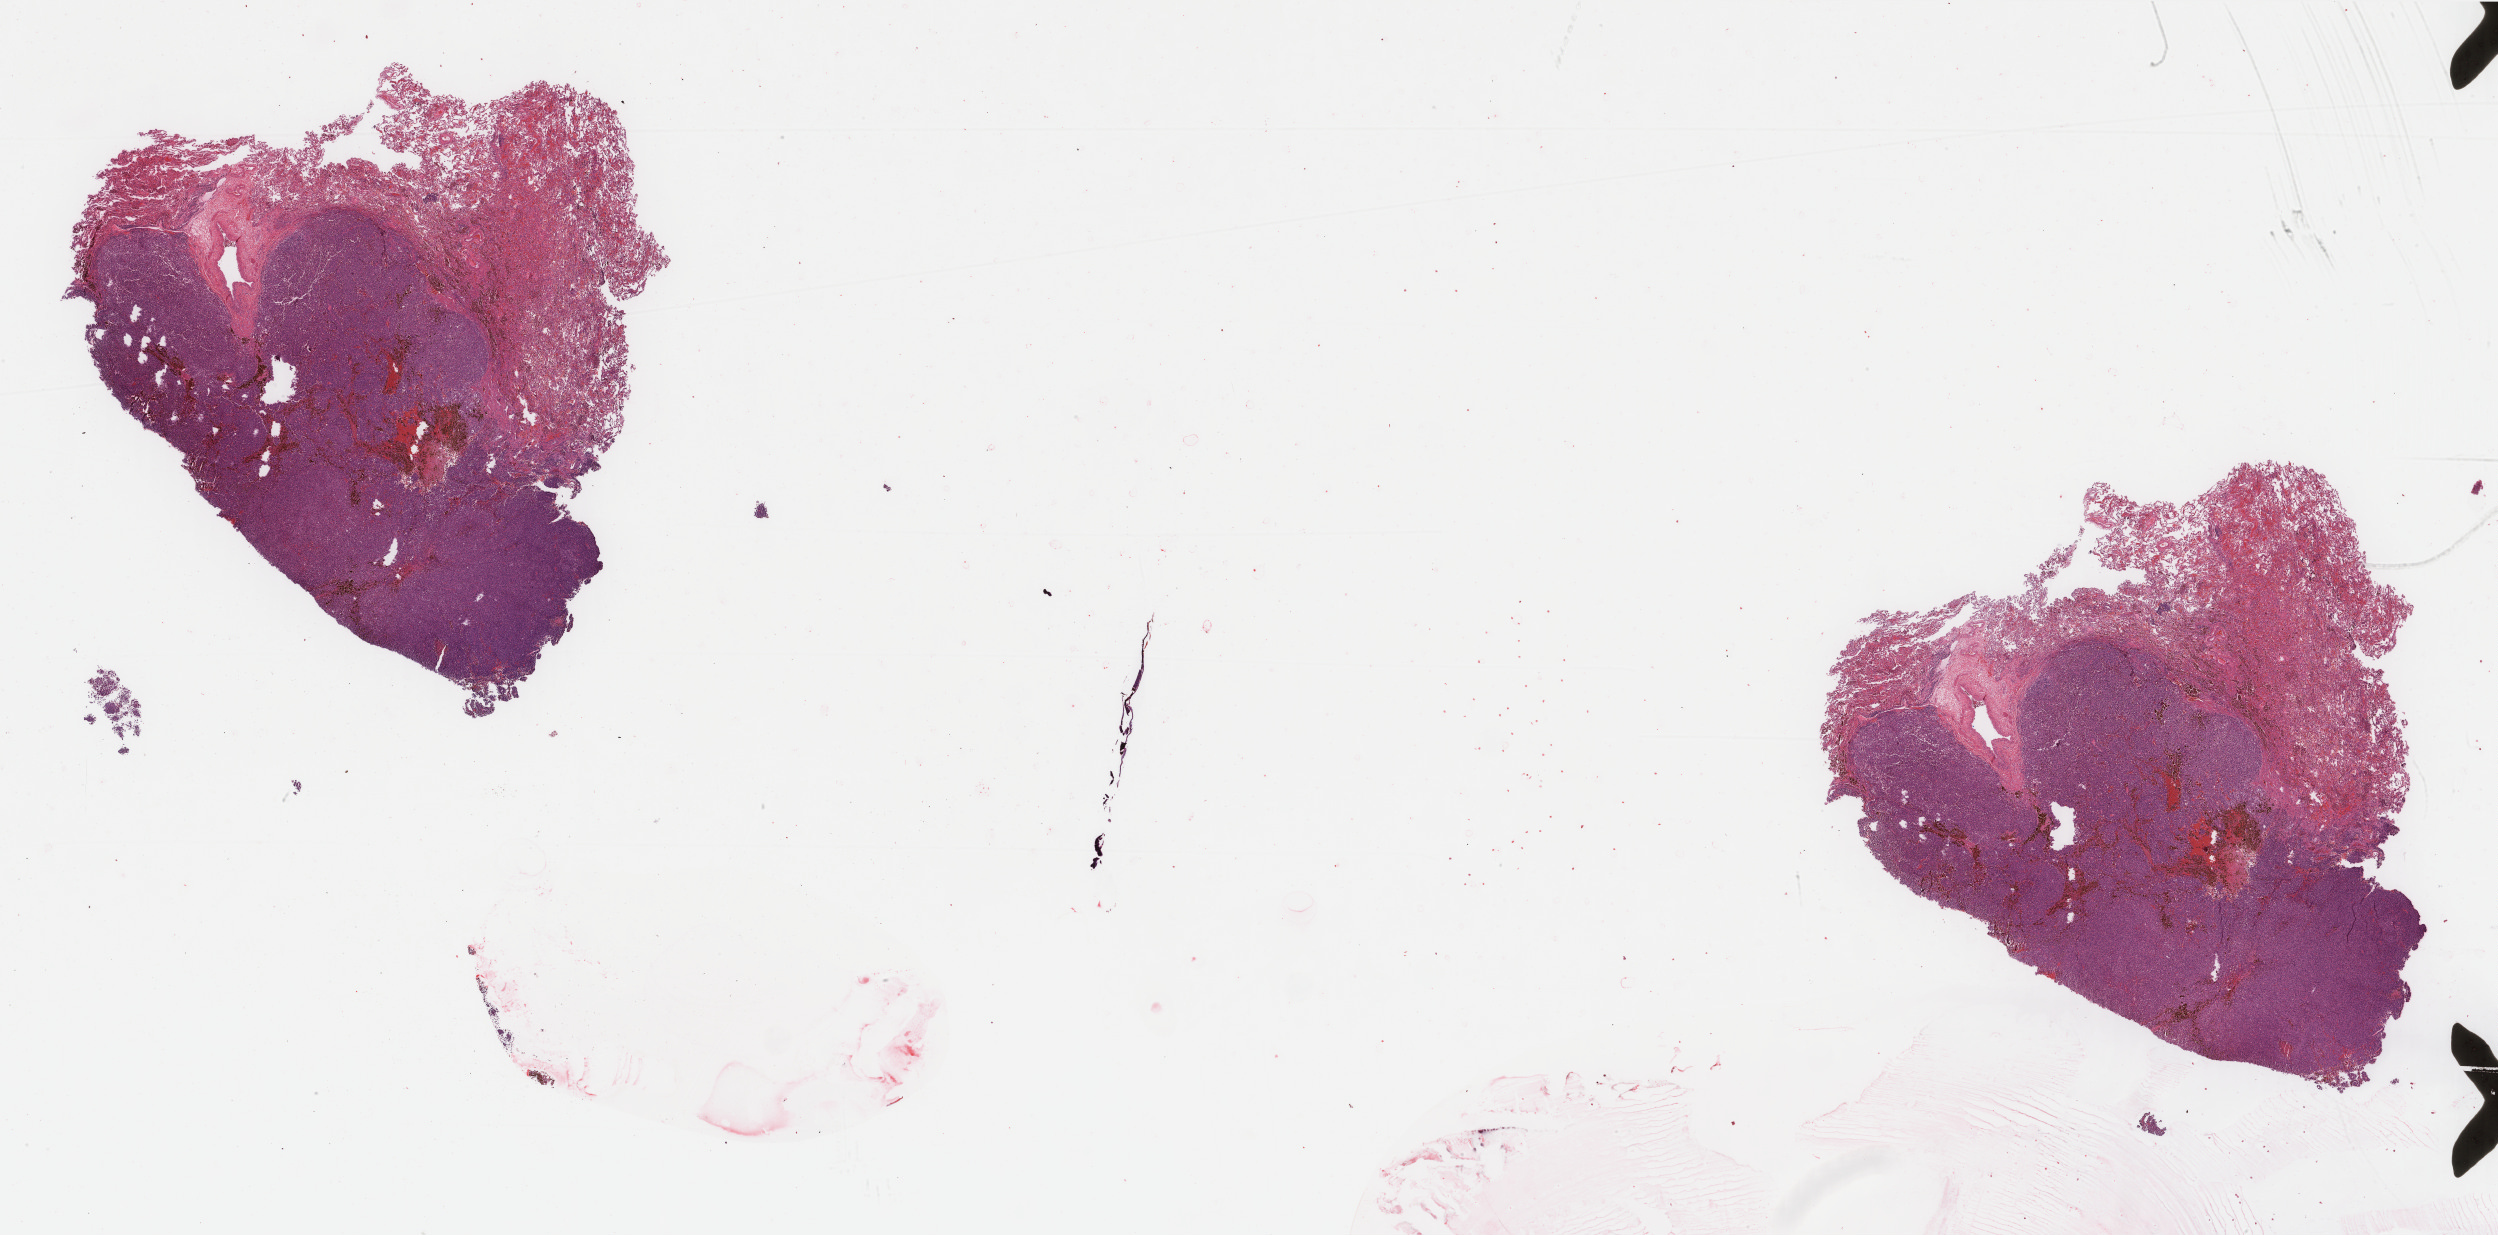
Digitized H&E-stained tissue section (whole slide), shown as a low-resolution overview of the whole scanned area (about 39.7 x 19.6 mm, from a 40x scan). Formalin-fixed paraffin-embedded (FFPE) diagnostic section. Skin, primary tumour sample. Patient: male, age at initial diagnosis 55 years.
- pathologic diagnosis: Malignant melanoma, NOS